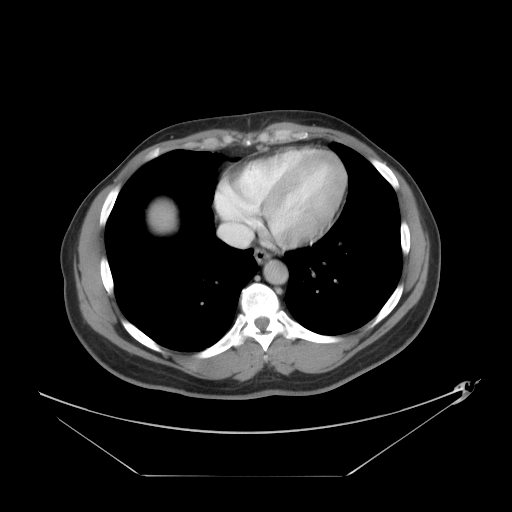
Contrast-enhanced abdominal CT, one axial slice; slice 41 of 44 in the series (ordered by position); reconstruction kernel STANDARD; intravenous contrast given; soft-tissue window (W 400 / L 40 HU); 5 mm slice thickness; 512 × 512 image matrix, field of view 466 × 466 mm. Male patient, age 49 years. Case-level facts recorded for this patient, not image findings: diagnosis: colorectal cancer liver metastases, imaged before liver resection; multiple liver metastases: no; largest metastasis: 8.5 cm; disease in both lobes: yes.
Outlined on this slice (outlined manually by an expert reader):
- liver: bounding box [x1, y1, x2, y2] px = [148, 199, 178, 234]